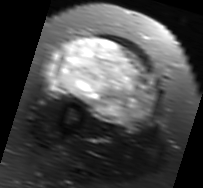
MRI of an extremity soft-tissue mass, one axial slice; position 33 of 91 along the scan axis; T2-weighted fat-saturated; MR volume resampled by the dataset authors to the PET/CT grid (not the native acquisition matrix); 3.27 mm slice thickness; 203 × 188 image matrix. Female patient. Case-level facts recorded for this patient, not image findings: histological type: malignant solitary fibrous tumor; grade: intermediate; site of the primary tumour: right thigh.
Structures marked on this image (expert contour drawn on MRI and transferred to this co-registered scan by the dataset authors):
- gross tumour volume including surrounding oedema: bounding box (x1, y1, x2, y2) in pixels: (42, 37, 159, 128)
- gross tumour volume (mass): (49, 37, 157, 125)